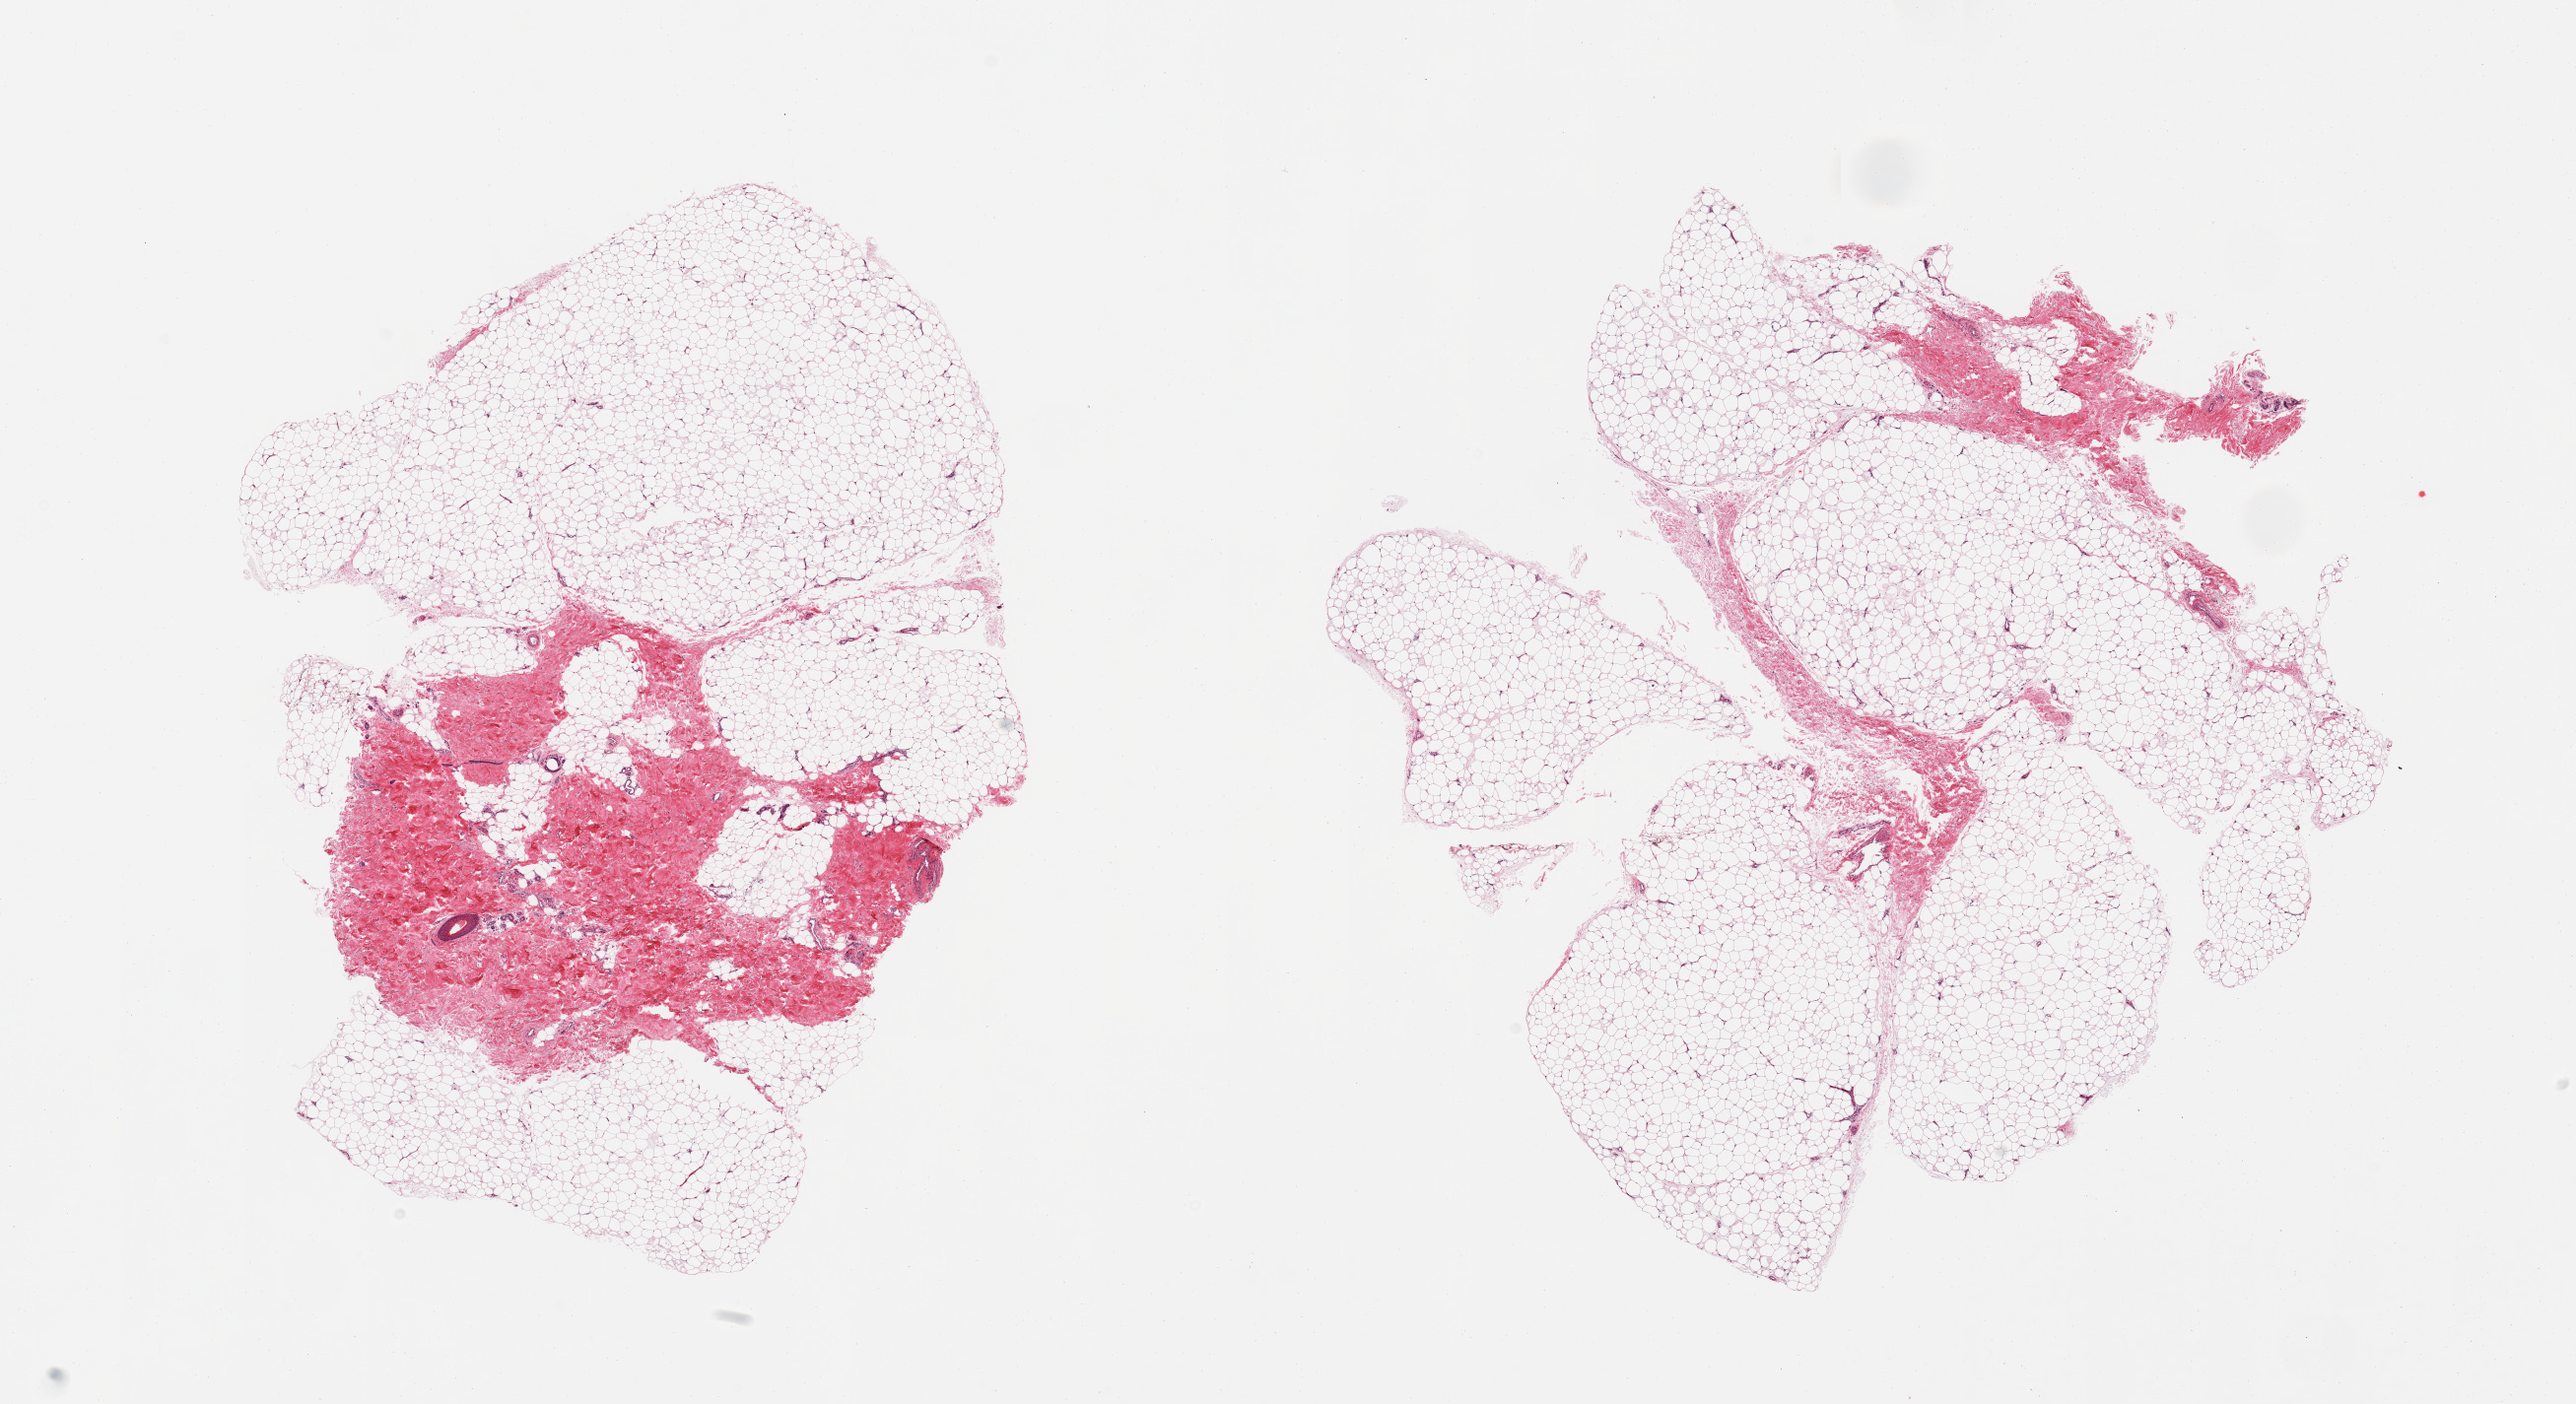
Whole-slide image, hematoxylin and eosin (H&E) stain, brightfield — low-resolution overview of the scanned area, about 20.7 x 11.3 mm (slide scanned at 20x), PAXgene-fixed paraffin-embedded (PFPE) section, section of adipose tissue (target tissue), donor tissue sample. Donor sex: female.
- reviewer comment on this tissue sample: 2 pieces; mature adiose tissue with 40% and 10% fibrovascular component